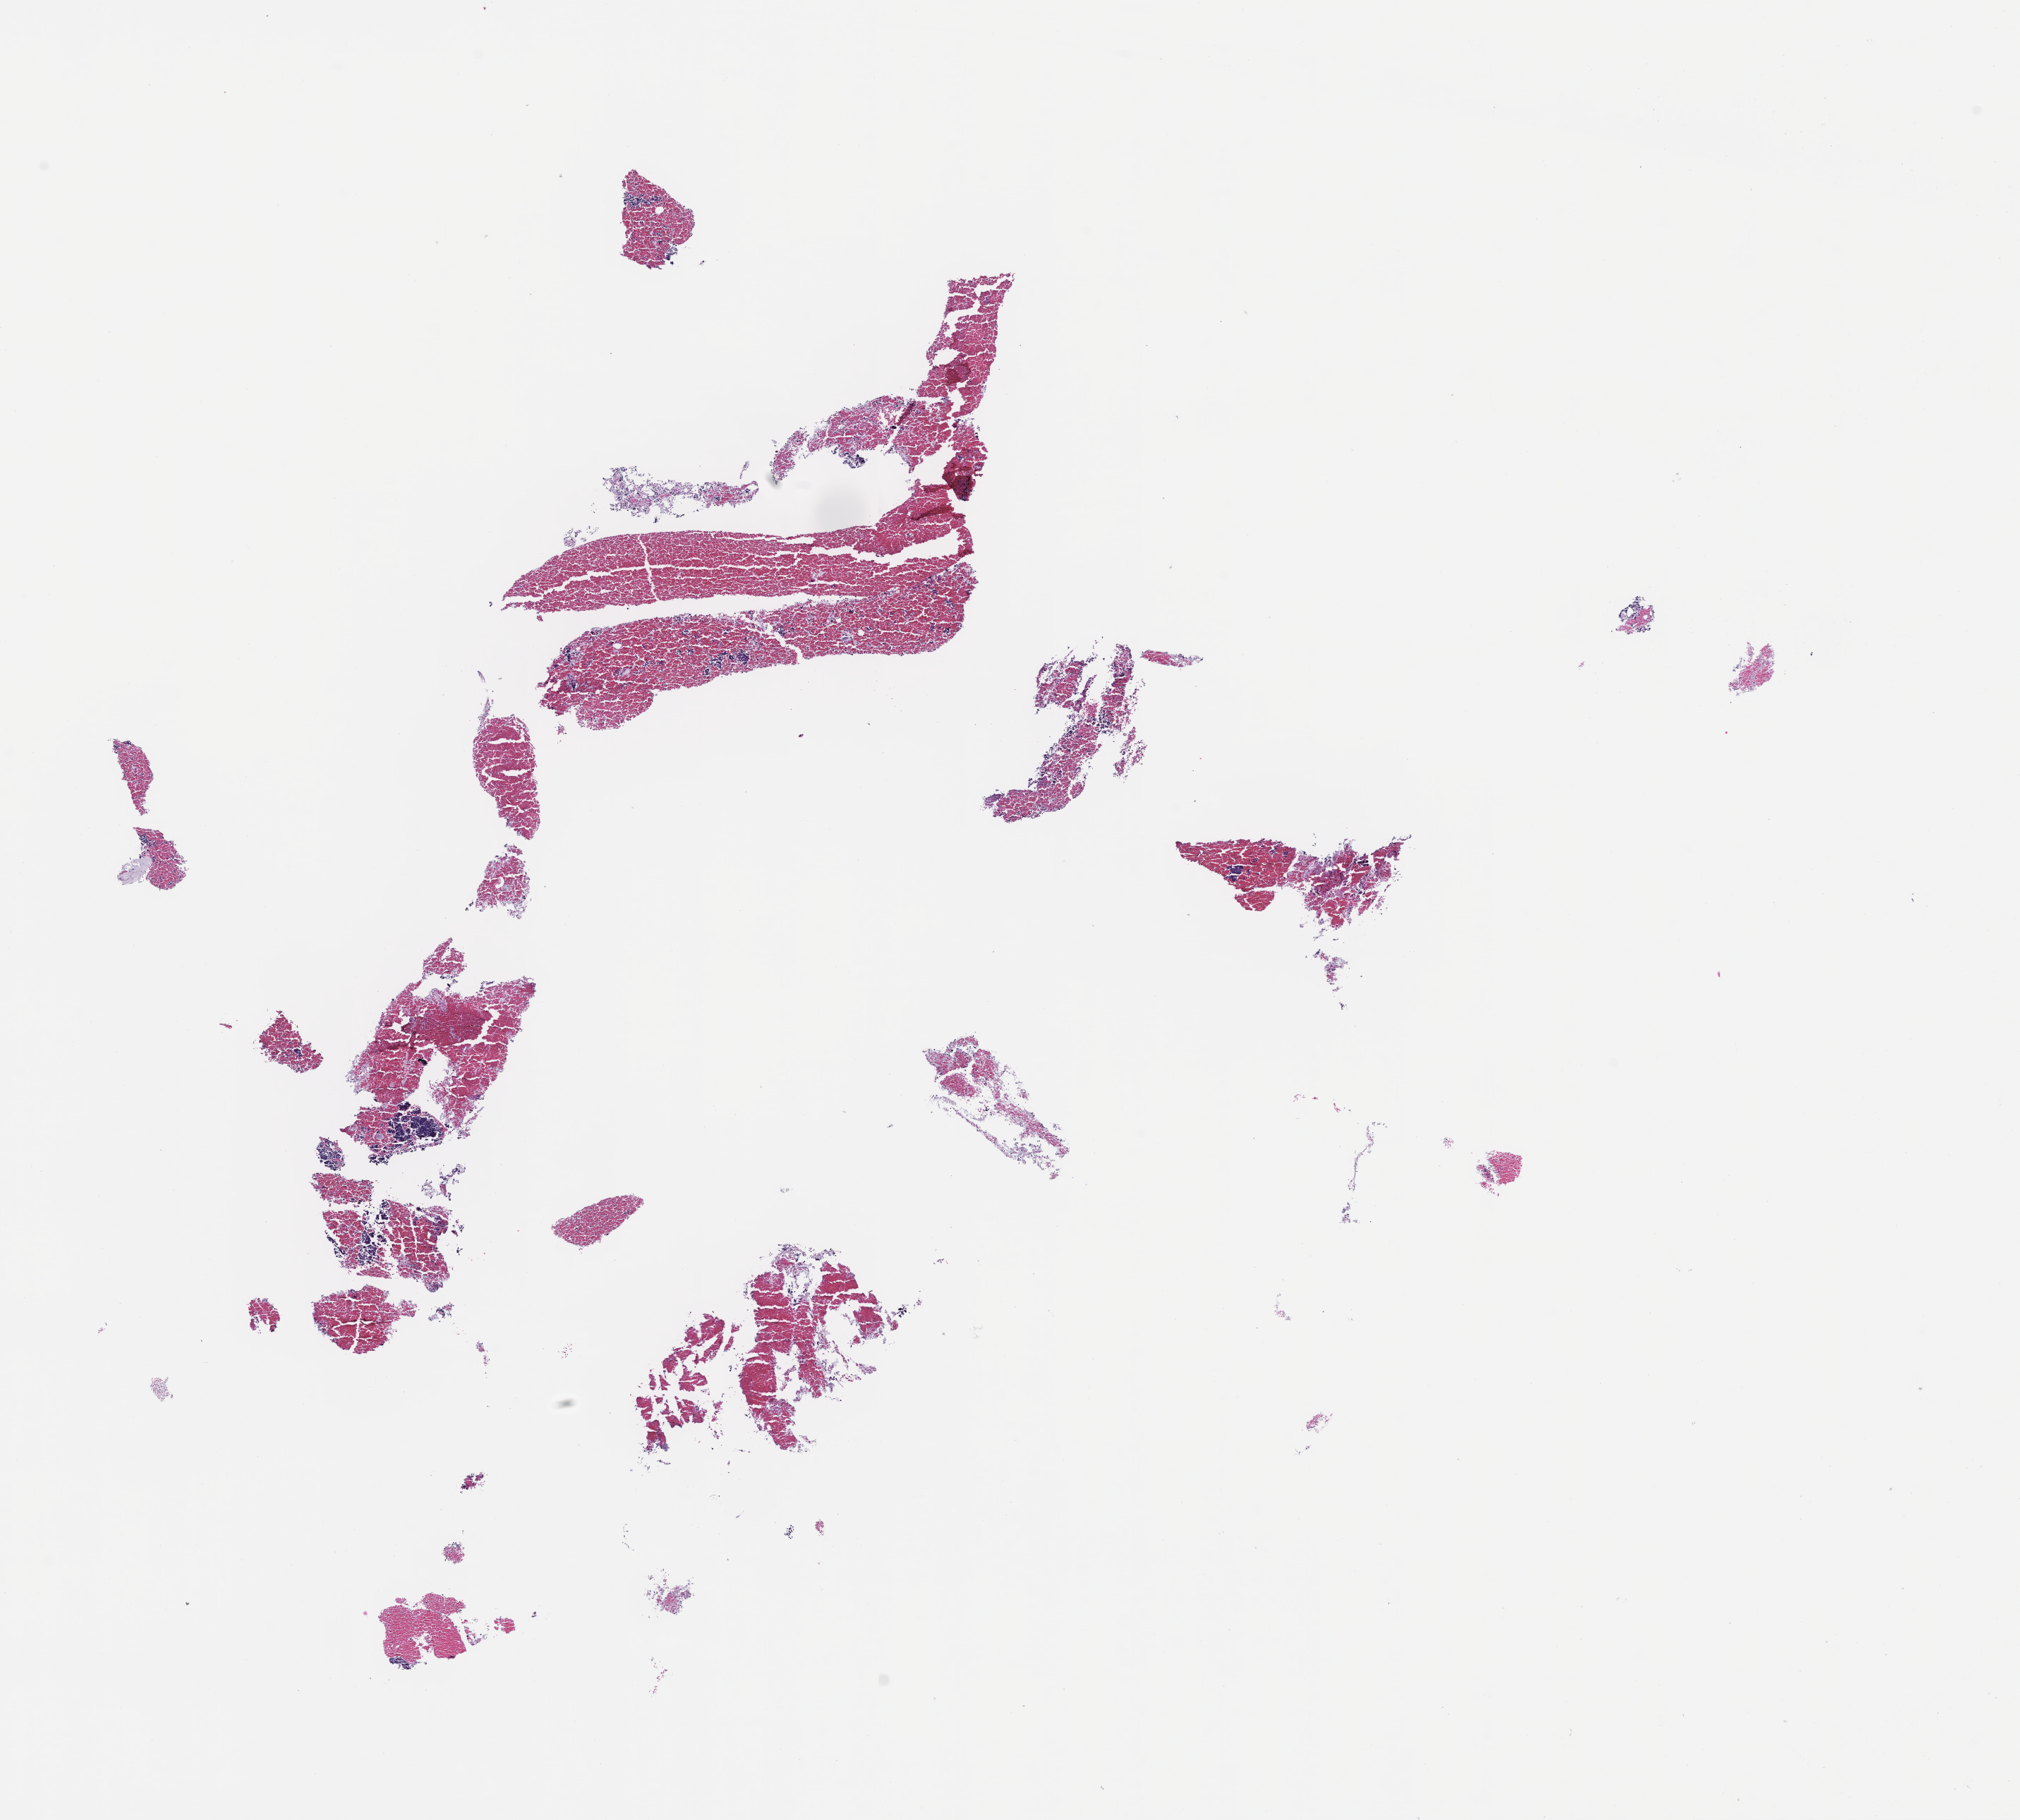
Hematoxylin and eosin (H&E) whole-slide image — whole scanned area (about 11.6 x 10.4 mm) shown as a low-resolution overview, formalin-fixed, paraffin-embedded (FFPE) tissue, specimen time point: archival tissue. Patient sex: male.
This section: metastatic tumor tissue. Patient diagnosis (primary): Small Cell Lung Carcinoma.